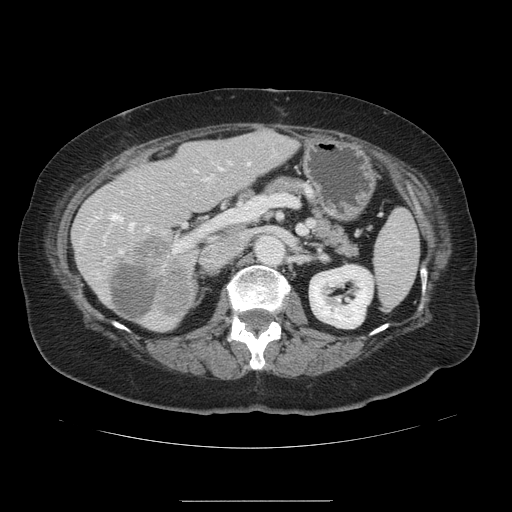
Contrast-enhanced abdominal CT, one axial slice; slice 65 of 141 in the series (ordered by position); 120 kVp; intravenous contrast given; soft-tissue window (W 400 / L 40 HU); 512 × 512 image matrix. Female patient, age 74 years. Case-level facts recorded for this patient, not image findings: diagnosis: colorectal cancer liver metastases, imaged before liver resection; multiple liver metastases: yes; largest metastasis: 7 cm.
Annotated regions visible in this slice (outlined manually by an expert reader):
- hepatic veins: bounding box (x1, y1, x2, y2) in pixels: (111, 186, 143, 234)
- liver: (73, 131, 296, 331)
- planned liver remnant (the part of the liver to remain after resection): (73, 131, 296, 331)
- portal vein (with intrahepatic branches): (118, 161, 250, 253)
- liver metastasis: (109, 264, 161, 322)
- liver metastasis: (131, 238, 194, 314)